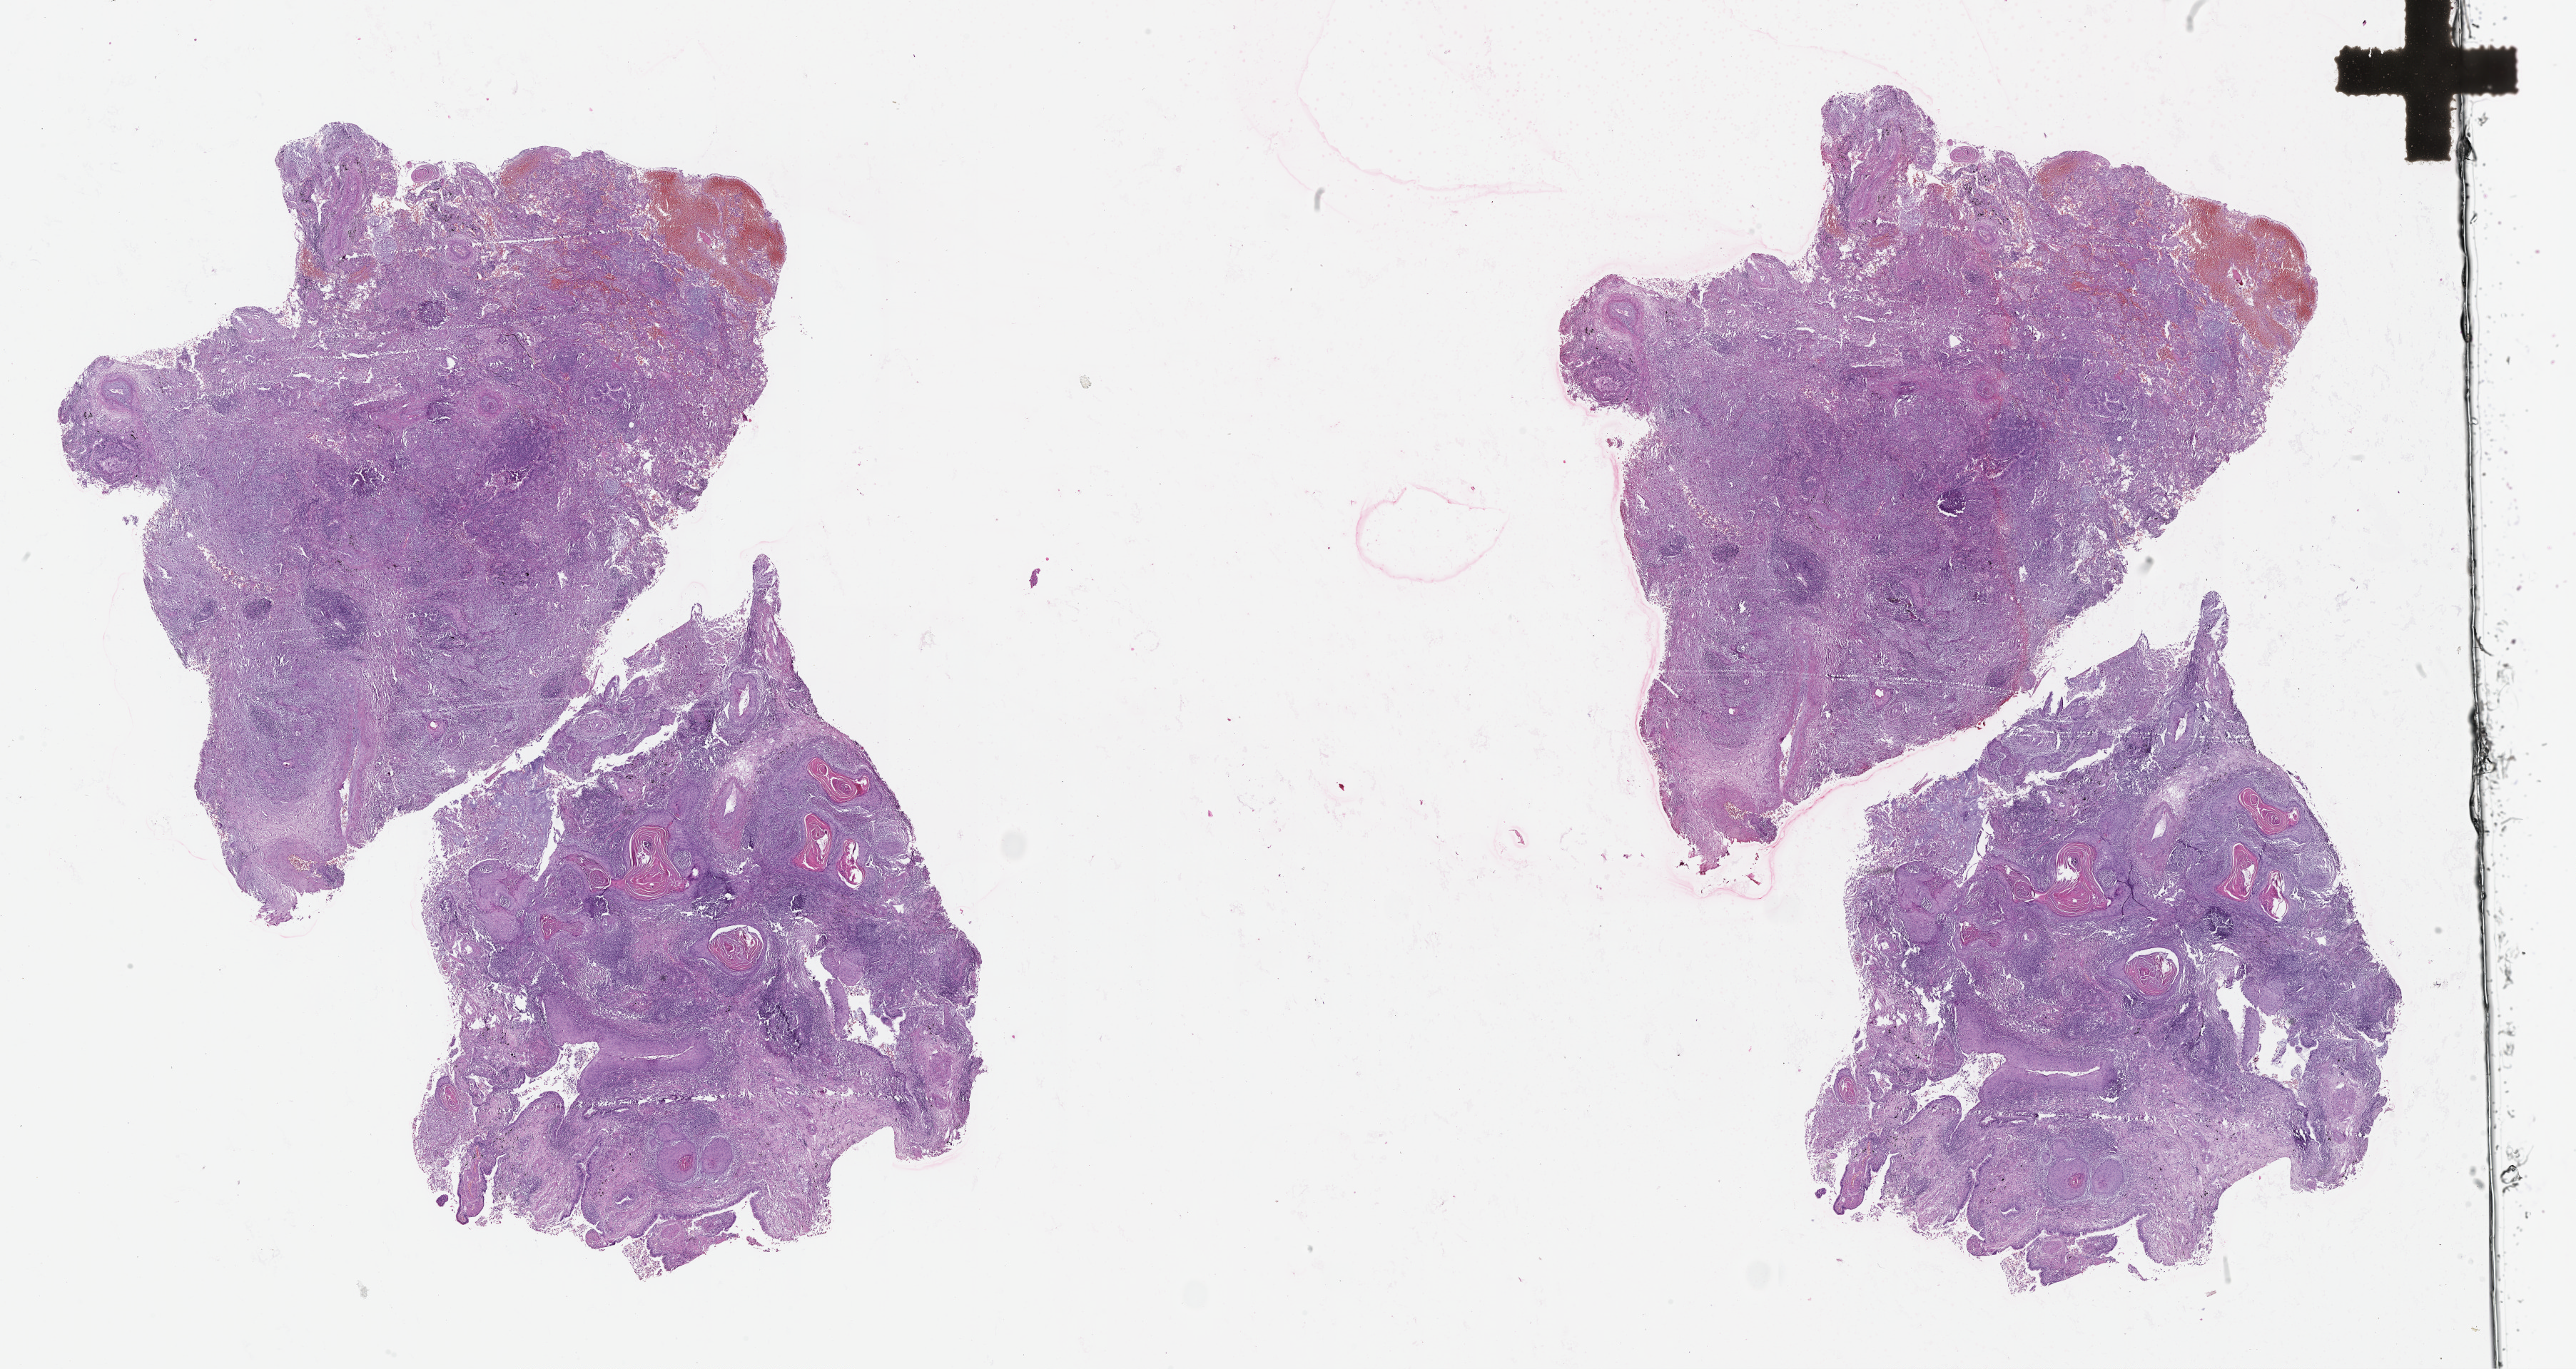
H&E-stained whole-slide image, a low-resolution overview of the entire scanned area, about 29.1 x 15.4 mm, tumour tissue sample, lung. Male, 72 y/o.
* patient diagnosis (cohort enrolment): squamous cell carcinoma (lung)